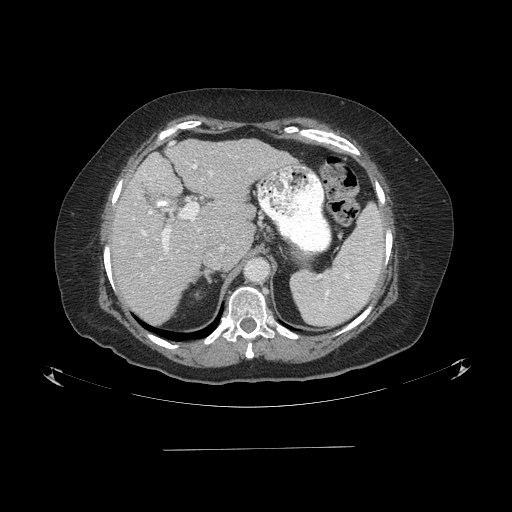
Contrast-enhanced abdominal CT (liver protocol), one axial slice. Slice 57 of 103 in the series (ordered by position). Reconstruction kernel STANDARD. 120 kVp. One of 2 acquisitions stored at this slice position. Soft-tissue window (W 400 / L 40 HU). 512 × 512 image matrix. Case-level facts recorded for this patient, not image findings: diagnosis: hepatocellular carcinoma (patient treated with transarterial chemoembolisation; whether this scan precedes or follows treatment is not stated here); TNM stage (as recorded): Stage-IIIA; Child-Pugh class: A; tumour size: 5.2 cm.
Structures marked on this image (semi-automatic segmentation, software-assisted and operator-edited):
- abdominal aorta: bounding box (x1, y1, x2, y2) in pixels: (245, 259, 267, 281)
- liver parenchyma outside the tumour (the mass and vessels are separate outlines, so this box may not span the whole liver): (110, 138, 294, 324)
- liver vessels: (139, 143, 213, 269)